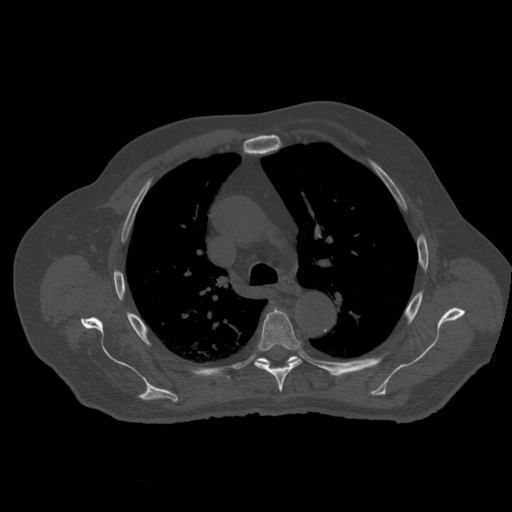
CT including the spine, one axial slice; position 396 of 399 along the scan axis; 120 kVp; bone window (W 1800 / L 400 HU); 1.25 mm slice thickness; 512 × 512 image matrix, field of view 407 × 407 mm. Patient age 73 years. From the clinical record (not read from this slice): primary cancer: prostate.
Structures marked on this image (semi-automatically segmented with operator editing):
- T5 vertebra: bounding box <255,310,302,393> (left, top, right, bottom; pixels)
- T6 vertebra: <257,356,298,366>